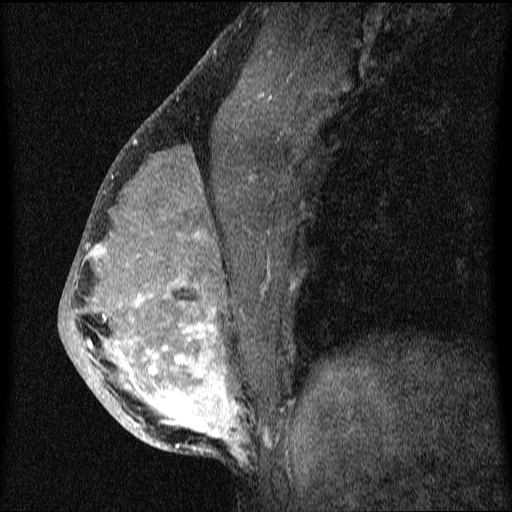
Breast MRI (dynamic contrast-enhanced), one sagittal slice; position 34 of 64 along the scan axis; dynamic contrast-enhanced series, image 2 of 4 at this slice position (ordered by acquisition); 1.5 T; TE 4.2 ms, TR 9.1 ms; 2 mm slice thickness; 512 × 512 image matrix. Patient: female, 33 years.
Structures marked on this image (semi-automatically segmented with operator editing):
- analysis volume of interest (the breast-tissue region the enhancement analysis was run in; not a lesion): bounding box (x1, y1, x2, y2) in pixels: (60, 151, 336, 458)
- tumour enhancement mask (voxels above the 70 % enhancement threshold inside the analysis volume of interest): (85, 234, 246, 458)